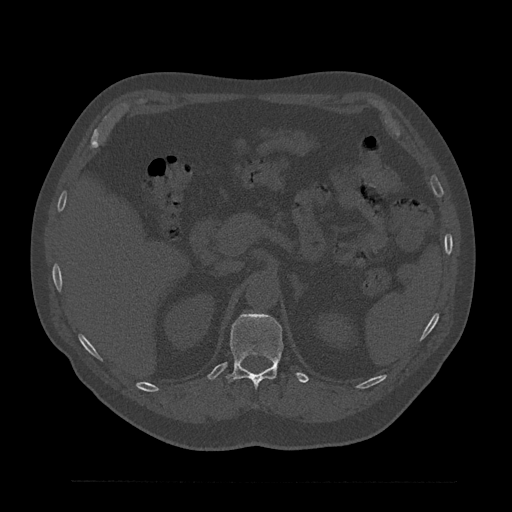
CT including the spine, one axial slice; slice 226 of 797 in the series (ordered by position); reconstruction kernel Br40s/3; 120 kVp; bone window (W 1800 / L 400 HU); 0.5 mm slice thickness; 512 × 512 image matrix, field of view 430 × 430 mm. Patient: male, 61 years. From the clinical record (not read from this slice): primary cancer: prostate.
Outlined on this slice (semi-automatically segmented with operator editing):
- T12 vertebra: box from (x=228, y=312) to (x=284, y=389) px